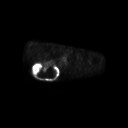
FDG PET of an extremity soft-tissue mass (from a PET/CT study), one axial slice. Slice 202 of 267 in the series (ordered by position). 128 × 128 image matrix, field of view 700 × 700 mm. Patient: male, 61 years. From the clinical record (not read from this slice): histological type: pleiomorphic spindle cell undifferentiated; grade: high; site of the primary tumour: right parascapusular.
Outlined on this slice (expert contour drawn on MRI and transferred to this co-registered scan by the dataset authors):
- gross tumour volume including surrounding oedema: bounding box (x1, y1, x2, y2) in pixels: (32, 62, 60, 78)
- gross tumour volume (mass): (32, 62, 58, 78)